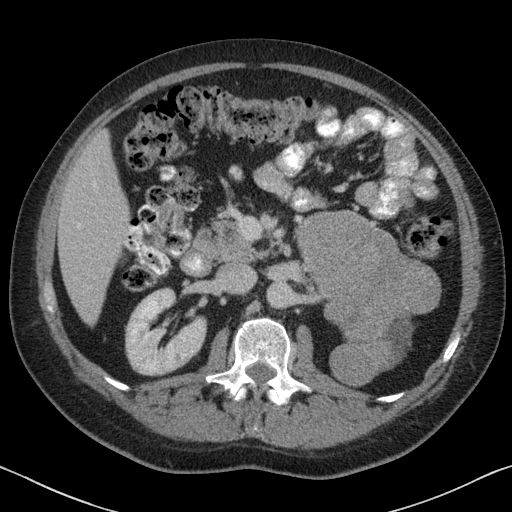
Contrast-enhanced abdominal CT, one axial slice. Reconstruction kernel B31f. Intravenous contrast given. Soft-tissue window (W 400 / L 40 HU). 3 mm slice thickness. 512 × 512 image matrix, field of view 366 × 366 mm. Male patient, age 51 years. From the clinical record (not read from this slice): diagnosis: adrenocortical carcinoma; tumour side: left adrenal; tumour size at pathology: 16.5 cm; Ki-67 index: 30 %; stage (as recorded): 2.
Annotated regions visible in this slice (semi-automatically segmented with operator editing):
- mass: bounding box <296,211,438,384> (left, top, right, bottom; pixels)